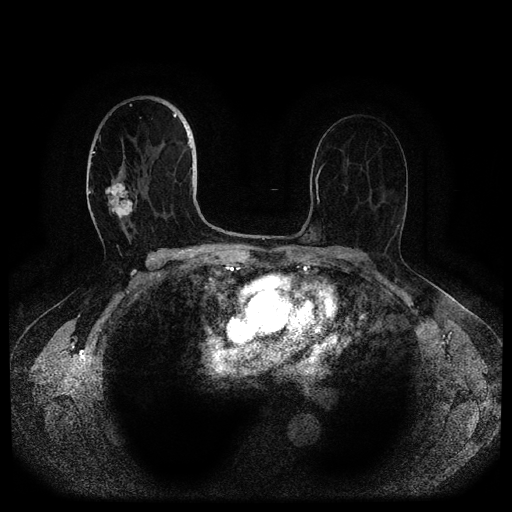
Breast MRI (dynamic contrast-enhanced, multi-phase), one axial slice. Slice 60 of 116 in the series (ordered by position). Dynamic contrast-enhanced series, time point 2 of 5 at this slice position (early post-contrast). 1.5 T. TE 2.6 ms, TR 5.3 ms. 2 mm slice thickness. 512 × 512 image matrix, field of view 350 × 350 mm. Female patient, age 82 years.
Structures marked on this image (semi-automatically segmented with operator editing):
- breast lesion (labelled 'tumour' in the annotation; benign lesions carry a separate 'benign' label): bounding box (x1, y1, x2, y2) in pixels: (105, 180, 133, 221)